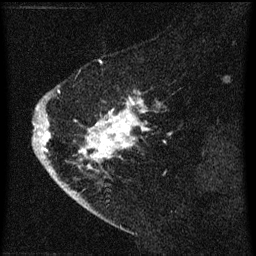
Breast MRI (dynamic contrast-enhanced), one sagittal slice; dynamic contrast-enhanced series, image 2 of 3 at this slice position (ordered by acquisition); 1.5 T; TE 4.2 ms, TR 8 ms; 2 mm slice thickness; 256 × 256 image matrix. Patient: female, 47 years.
Outlined on this slice (semi-automatically segmented with operator editing):
- analysis volume of interest (the breast-tissue region the enhancement analysis was run in; not a lesion): bounding box (x1, y1, x2, y2) in pixels: (38, 76, 164, 193)
- tumour enhancement mask (voxels above the 70 % enhancement threshold inside the analysis volume of interest): (38, 92, 159, 193)